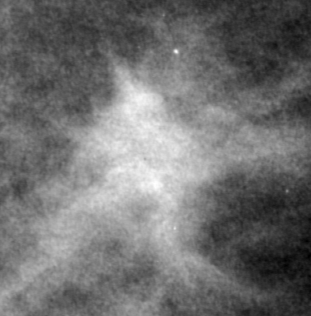
Crop from a digitized film mammogram around one marked abnormality, right breast, CC view, BI-RADS breast density category 3 (scale 1–4).
- Marked abnormality: mass, shape irregular, margins spiculated; BI-RADS assessment category 5; pathology result (as recorded, not read from the image): malignant.